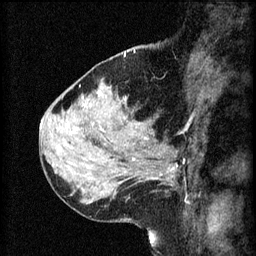
Breast MRI (dynamic contrast-enhanced), one sagittal slice. Position 25 of 60 along the scan axis. 3 images stored at this slice position (order not interpretable as contrast timing). 1.5 T. TE 4.2 ms, TR 8.2 ms. 2 mm slice thickness. 256 × 256 image matrix. Patient: female, 37 years.
Annotated regions visible in this slice (semi-automatic segmentation, software-assisted and operator-edited):
- analysis volume of interest (the breast-tissue region the enhancement analysis was run in; not a lesion): bounding box <124,138,190,191> (left, top, right, bottom; pixels)
- tumour enhancement mask (voxels above the 70 % enhancement threshold inside the analysis volume of interest): <146,166,178,181>